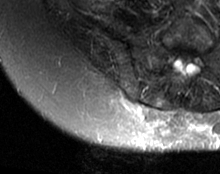
MRI of an extremity soft-tissue mass, one axial slice; T2-weighted fat-saturated; MR volume resampled by the dataset authors to the PET/CT grid (not the native acquisition matrix); 220 × 174 image matrix. Female patient. From the clinical record (not read from this slice): histological type: spindle cell suggestive of myxofibrosarcoma; grade: intermediate; site of the primary tumour: right buttock.
Outlined on this slice (expert contour drawn on MRI and transferred to this co-registered scan by the dataset authors):
- gross tumour volume (mass): bounding box <118,97,172,128> (left, top, right, bottom; pixels)